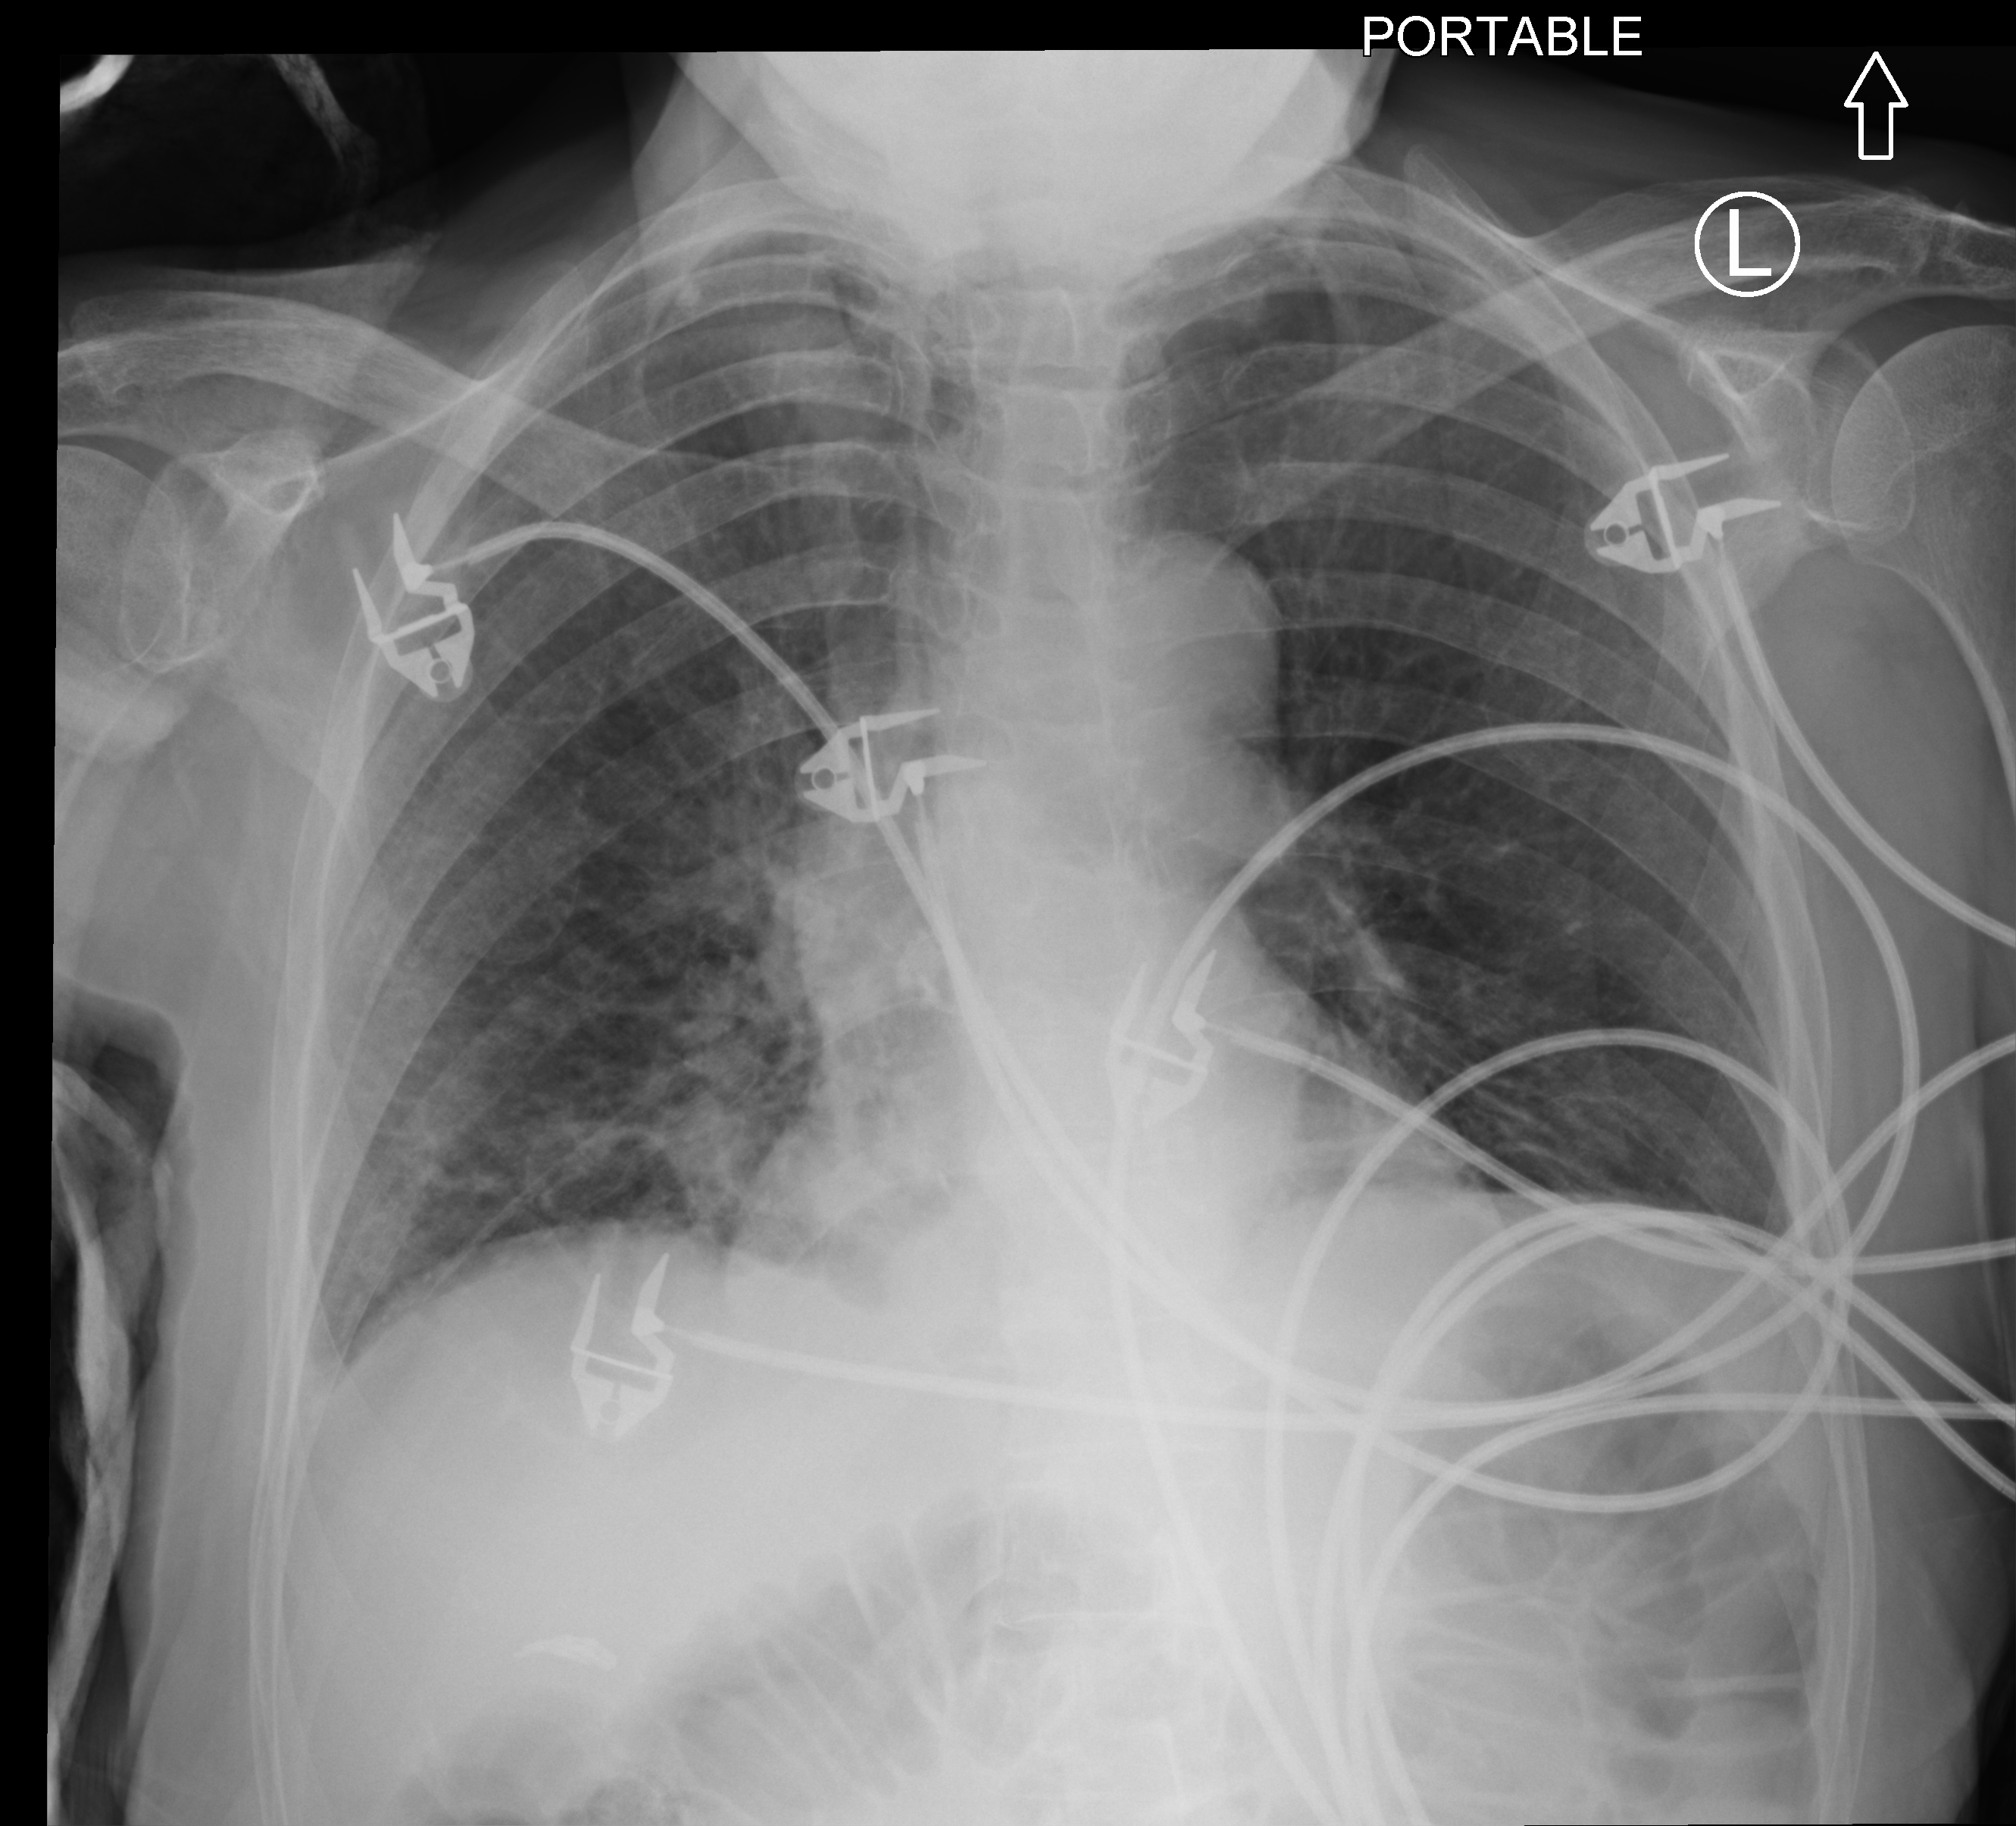
Chest X-ray (portable); anteroposterior (AP) projection. Female patient hospitalised with COVID-19, age 75–90 years.
From the hospital-stay record, not from the radiograph (when in the stay this image was taken is not recorded): mechanically ventilated during this hospital stay: no.